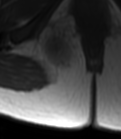
MRI of an extremity soft-tissue mass, one axial slice; slice 30 of 47 in the series (ordered by position); MR volume resampled by the dataset authors to the PET/CT grid (not the native acquisition matrix); 3.27 mm slice thickness; 121 × 139 image matrix, field of view 118 × 136 mm. Female patient. From the clinical record (not read from this slice): histological type: epithelioid sarcoma; grade: intermediate; site of the primary tumour: right buttock.
Annotated regions visible in this slice (expert contour drawn on MRI and transferred to this co-registered scan by the dataset authors):
- gross tumour volume including surrounding oedema: bounding box [x1, y1, x2, y2] px = [38, 25, 78, 74]
- gross tumour volume (mass): [41, 32, 71, 69]